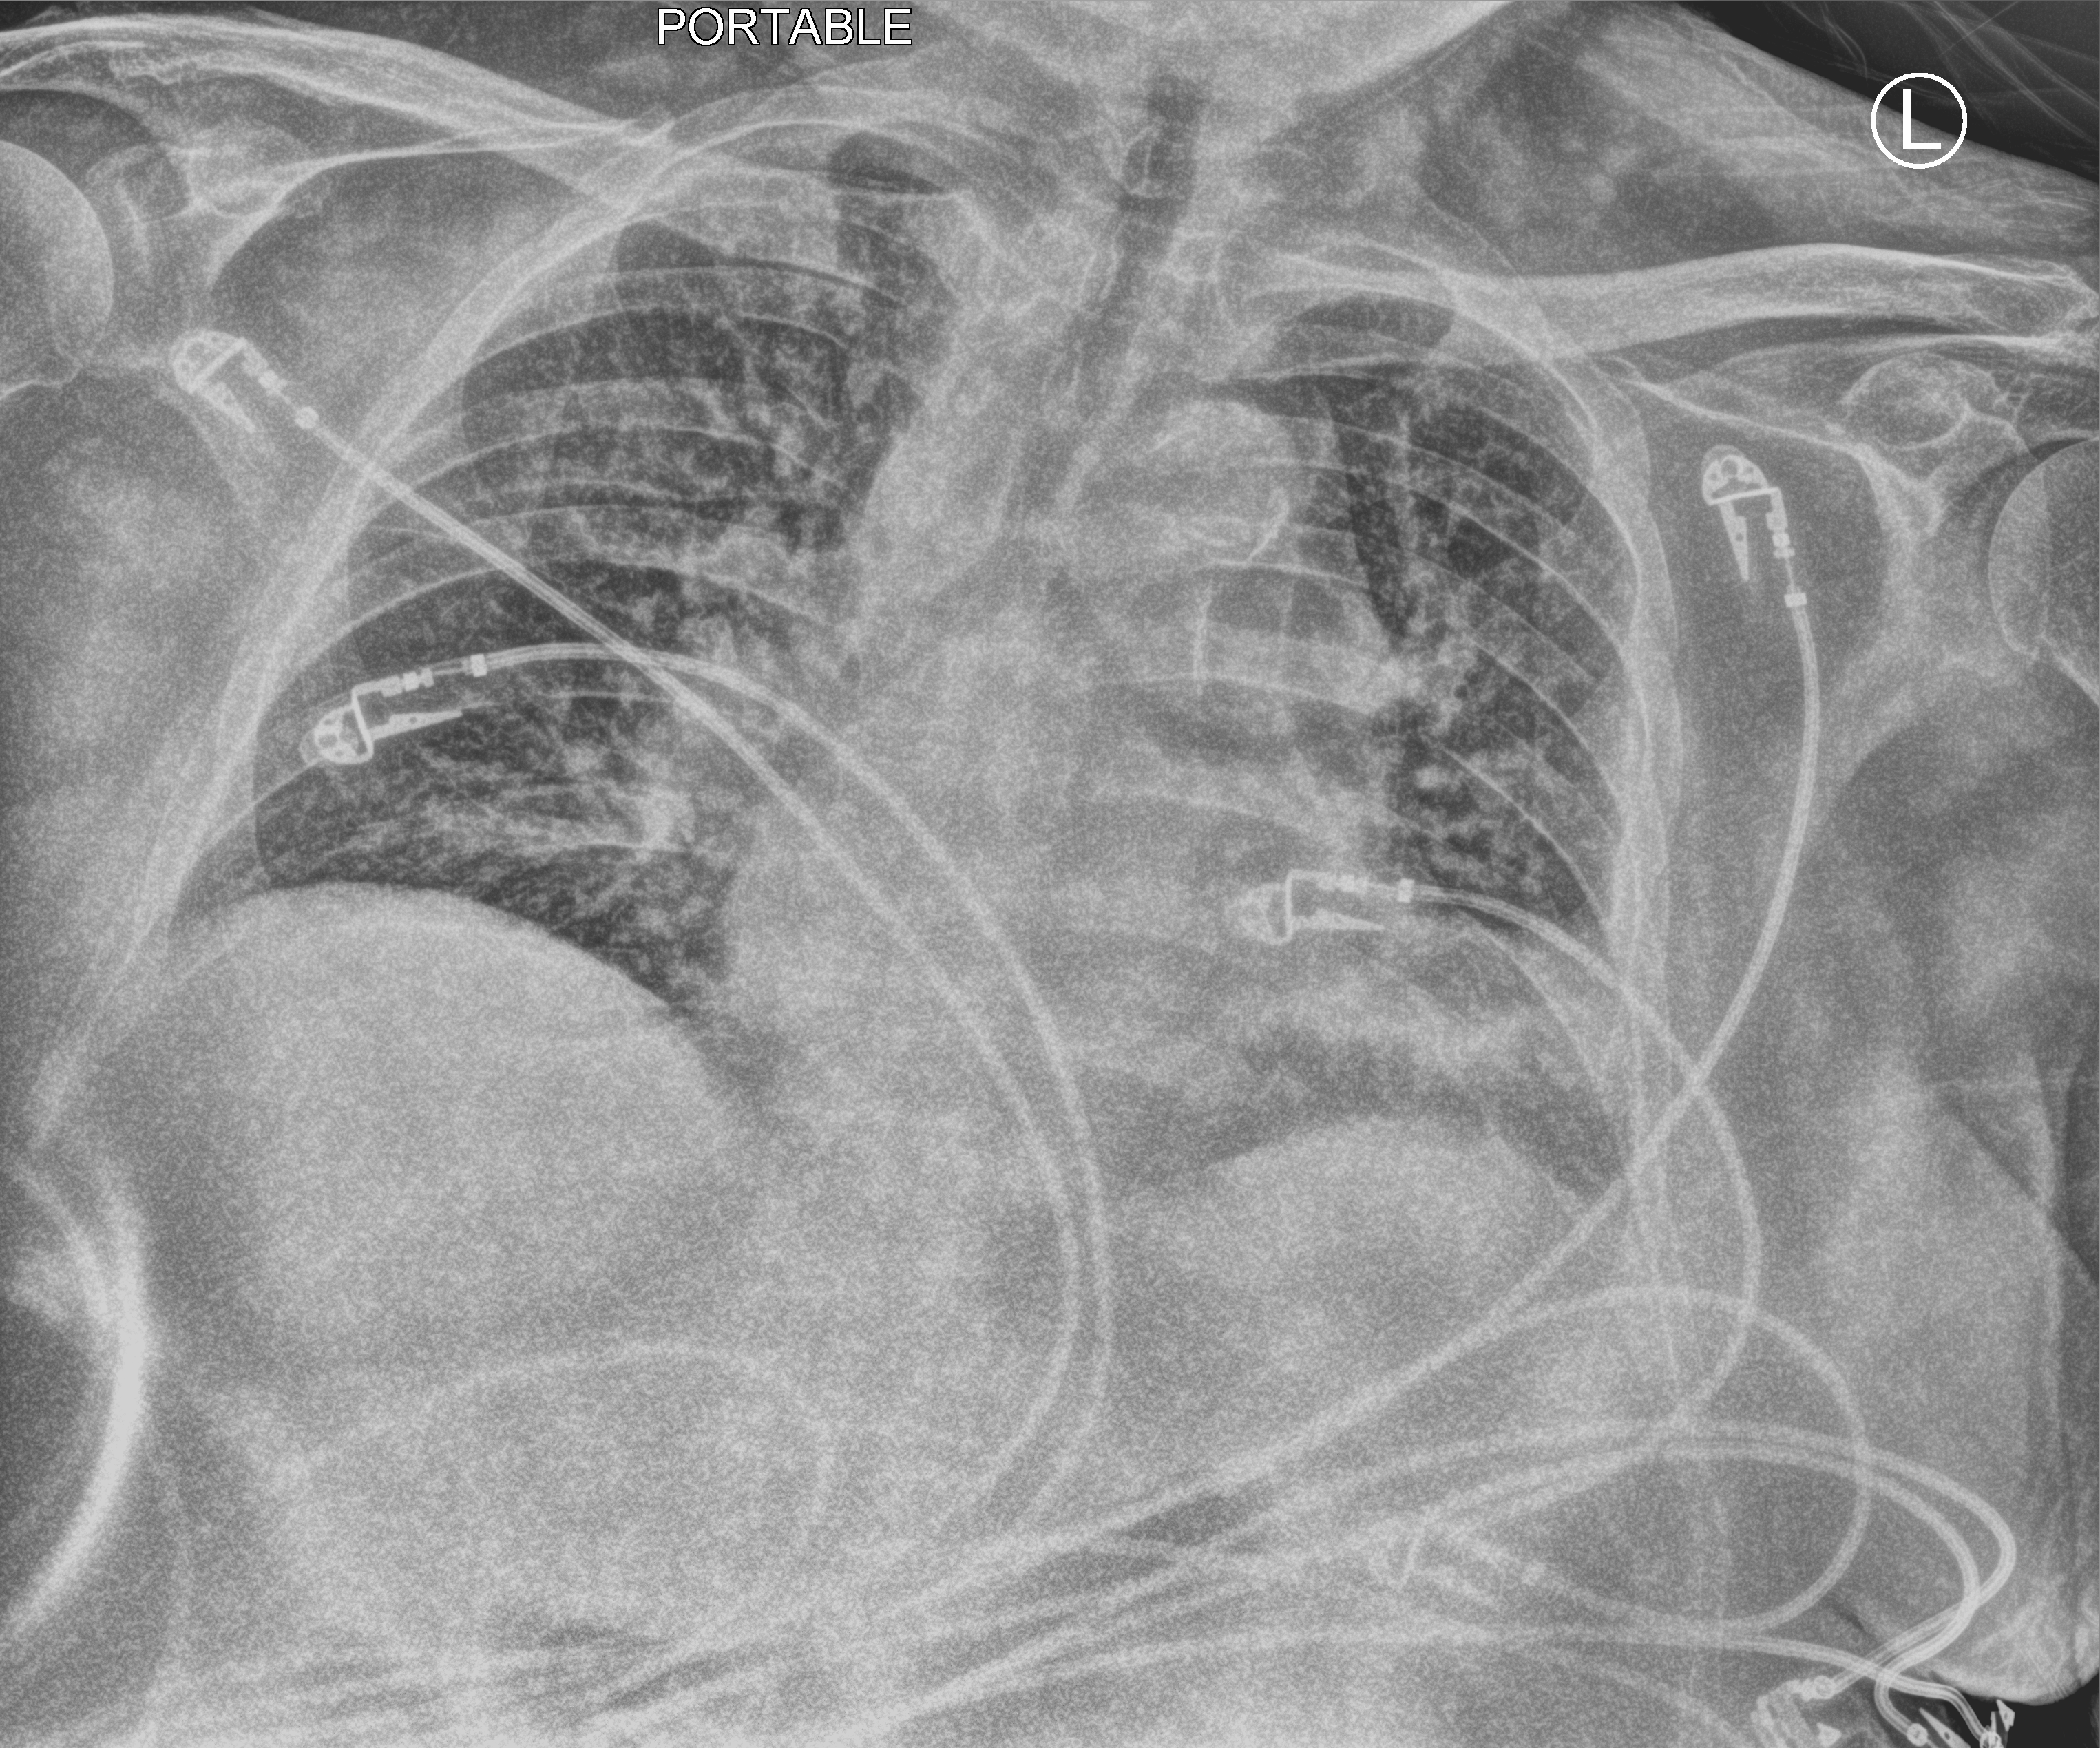
Bedside chest radiograph (computed radiography), anteroposterior (AP) projection. Male patient hospitalised with COVID-19, age 75–90 years.
Hospital-stay facts (about this admission, not read from this image; timing relative to this image not recorded):
- mechanically ventilated during this hospital stay: no
- admitted to intensive care during this hospital stay: no